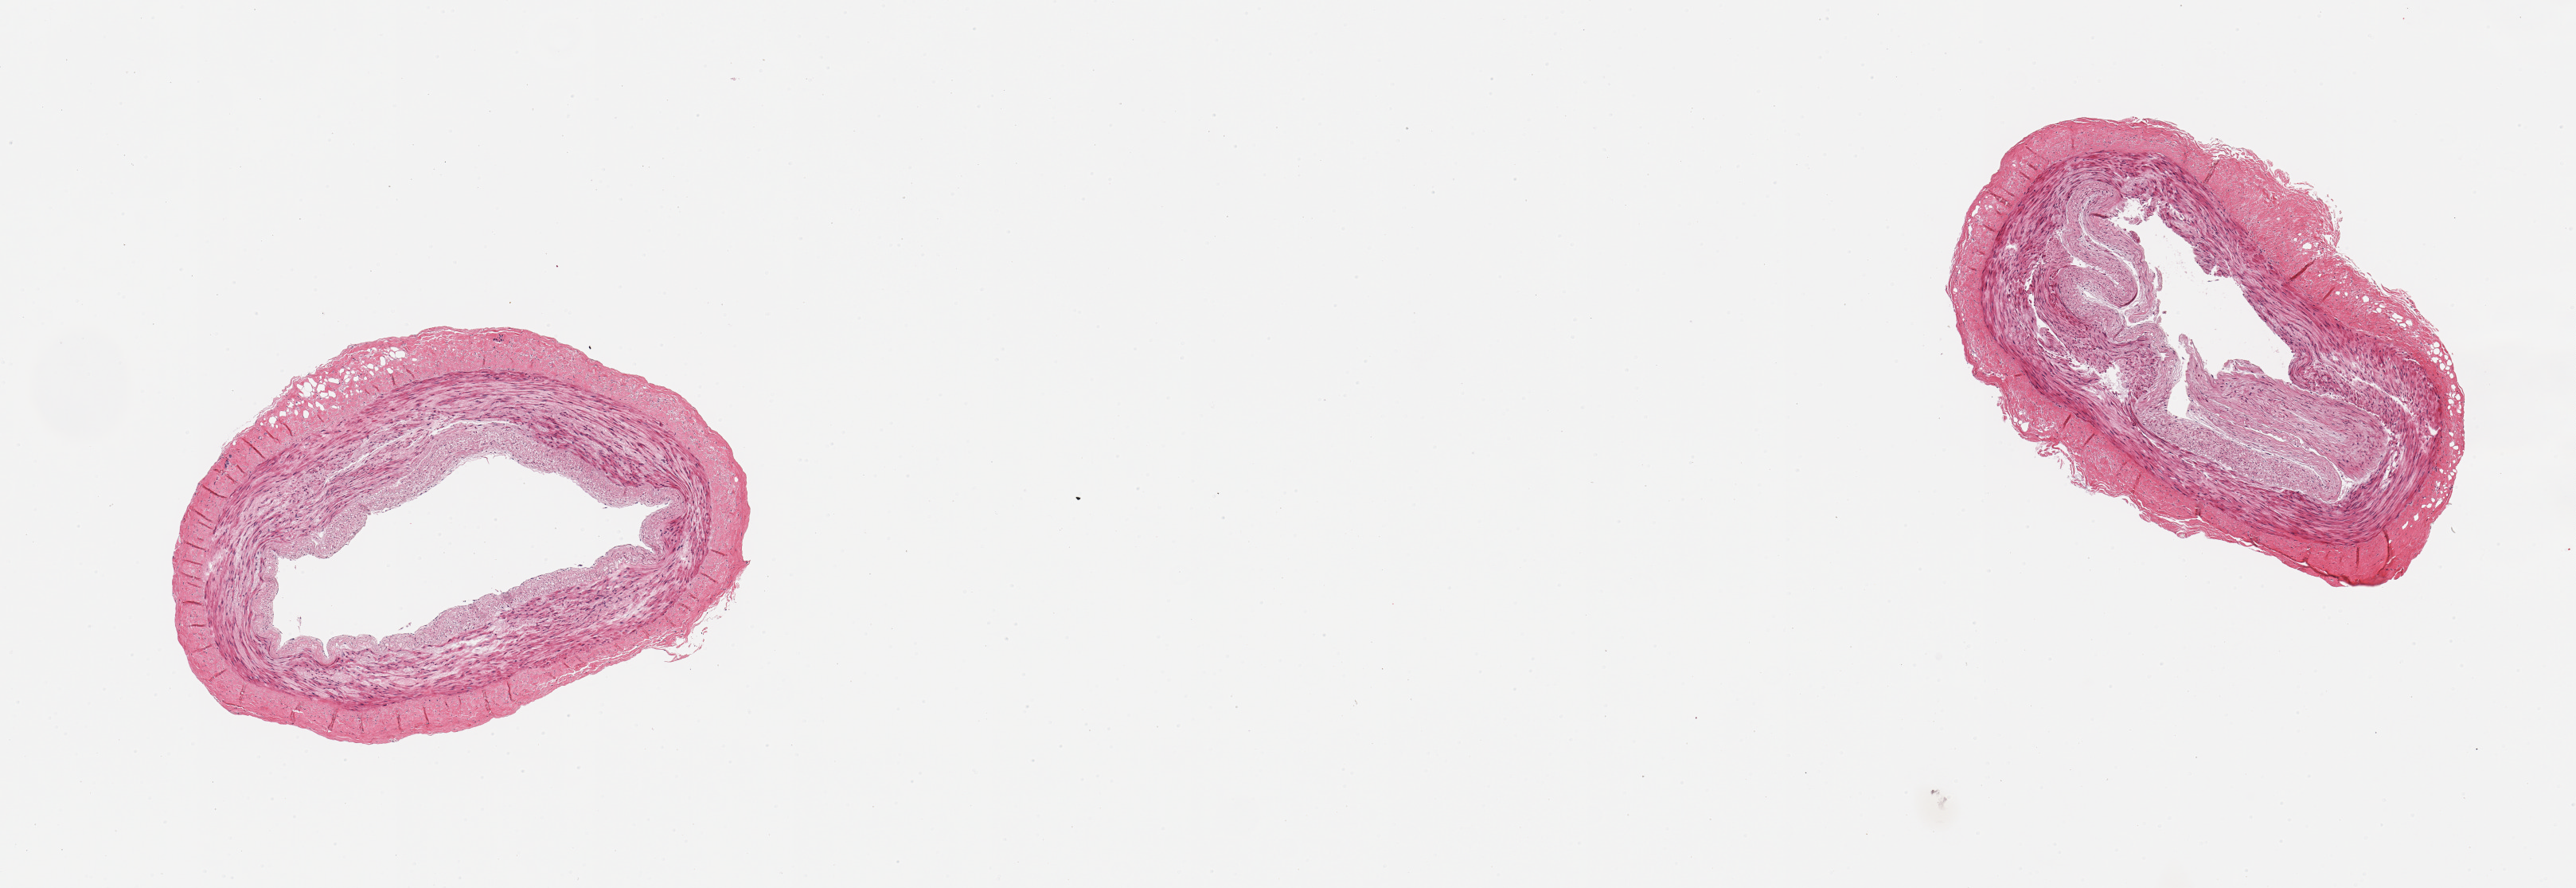
Digitized haematoxylin and eosin-stained section, brightfield, a low-resolution overview of the entire scanned area, about 12.8 x 4.4 mm (from a 20x scan); PAXgene-fixed, paraffin-embedded tissue; sampled site (target tissue): tibial artery; donor tissue sample. Female donor.
Reviewer comment on this tissue sample: 2 pieces; no plaques; well trimmed.